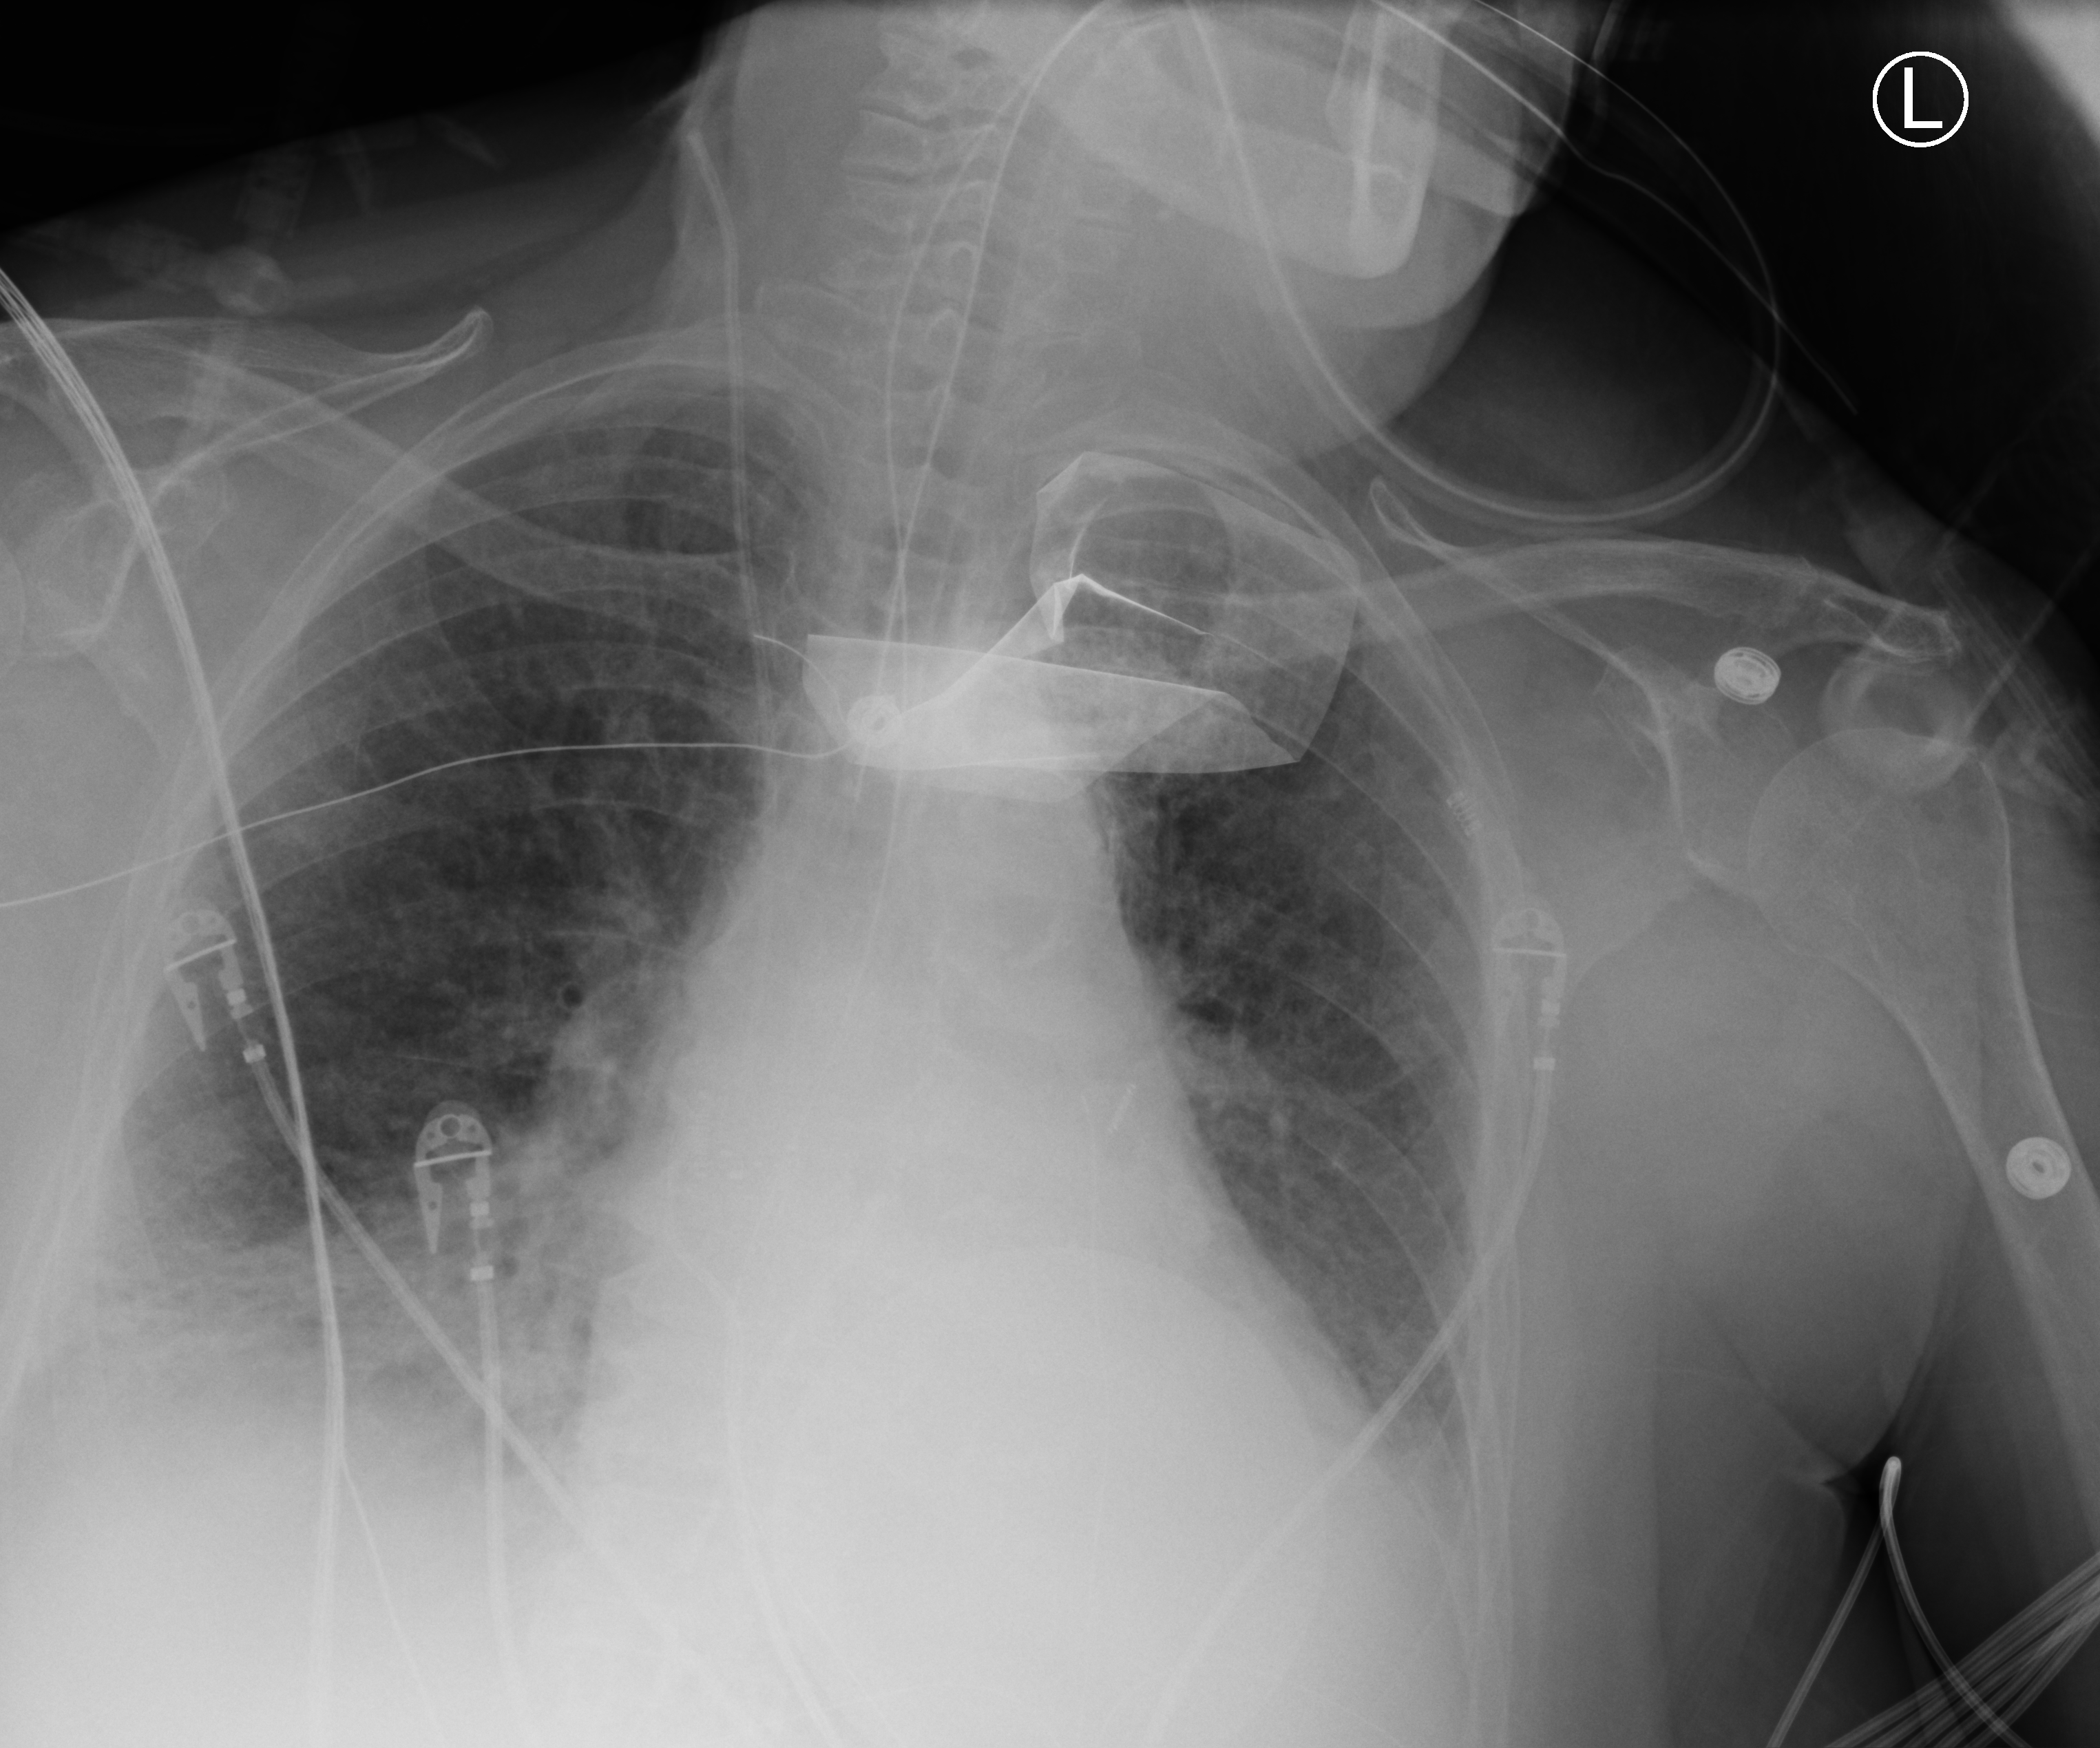
Bedside chest radiograph (computed radiography); anteroposterior (AP) projection. Patient hospitalised with COVID-19; female, aged 75–90 years.
Admission-level facts for this patient (not findings on this image; timing relative to this image not recorded):
- chronic kidney disease (admission record): yes
- length of hospital stay: 10 days
- diabetes (admission record): yes